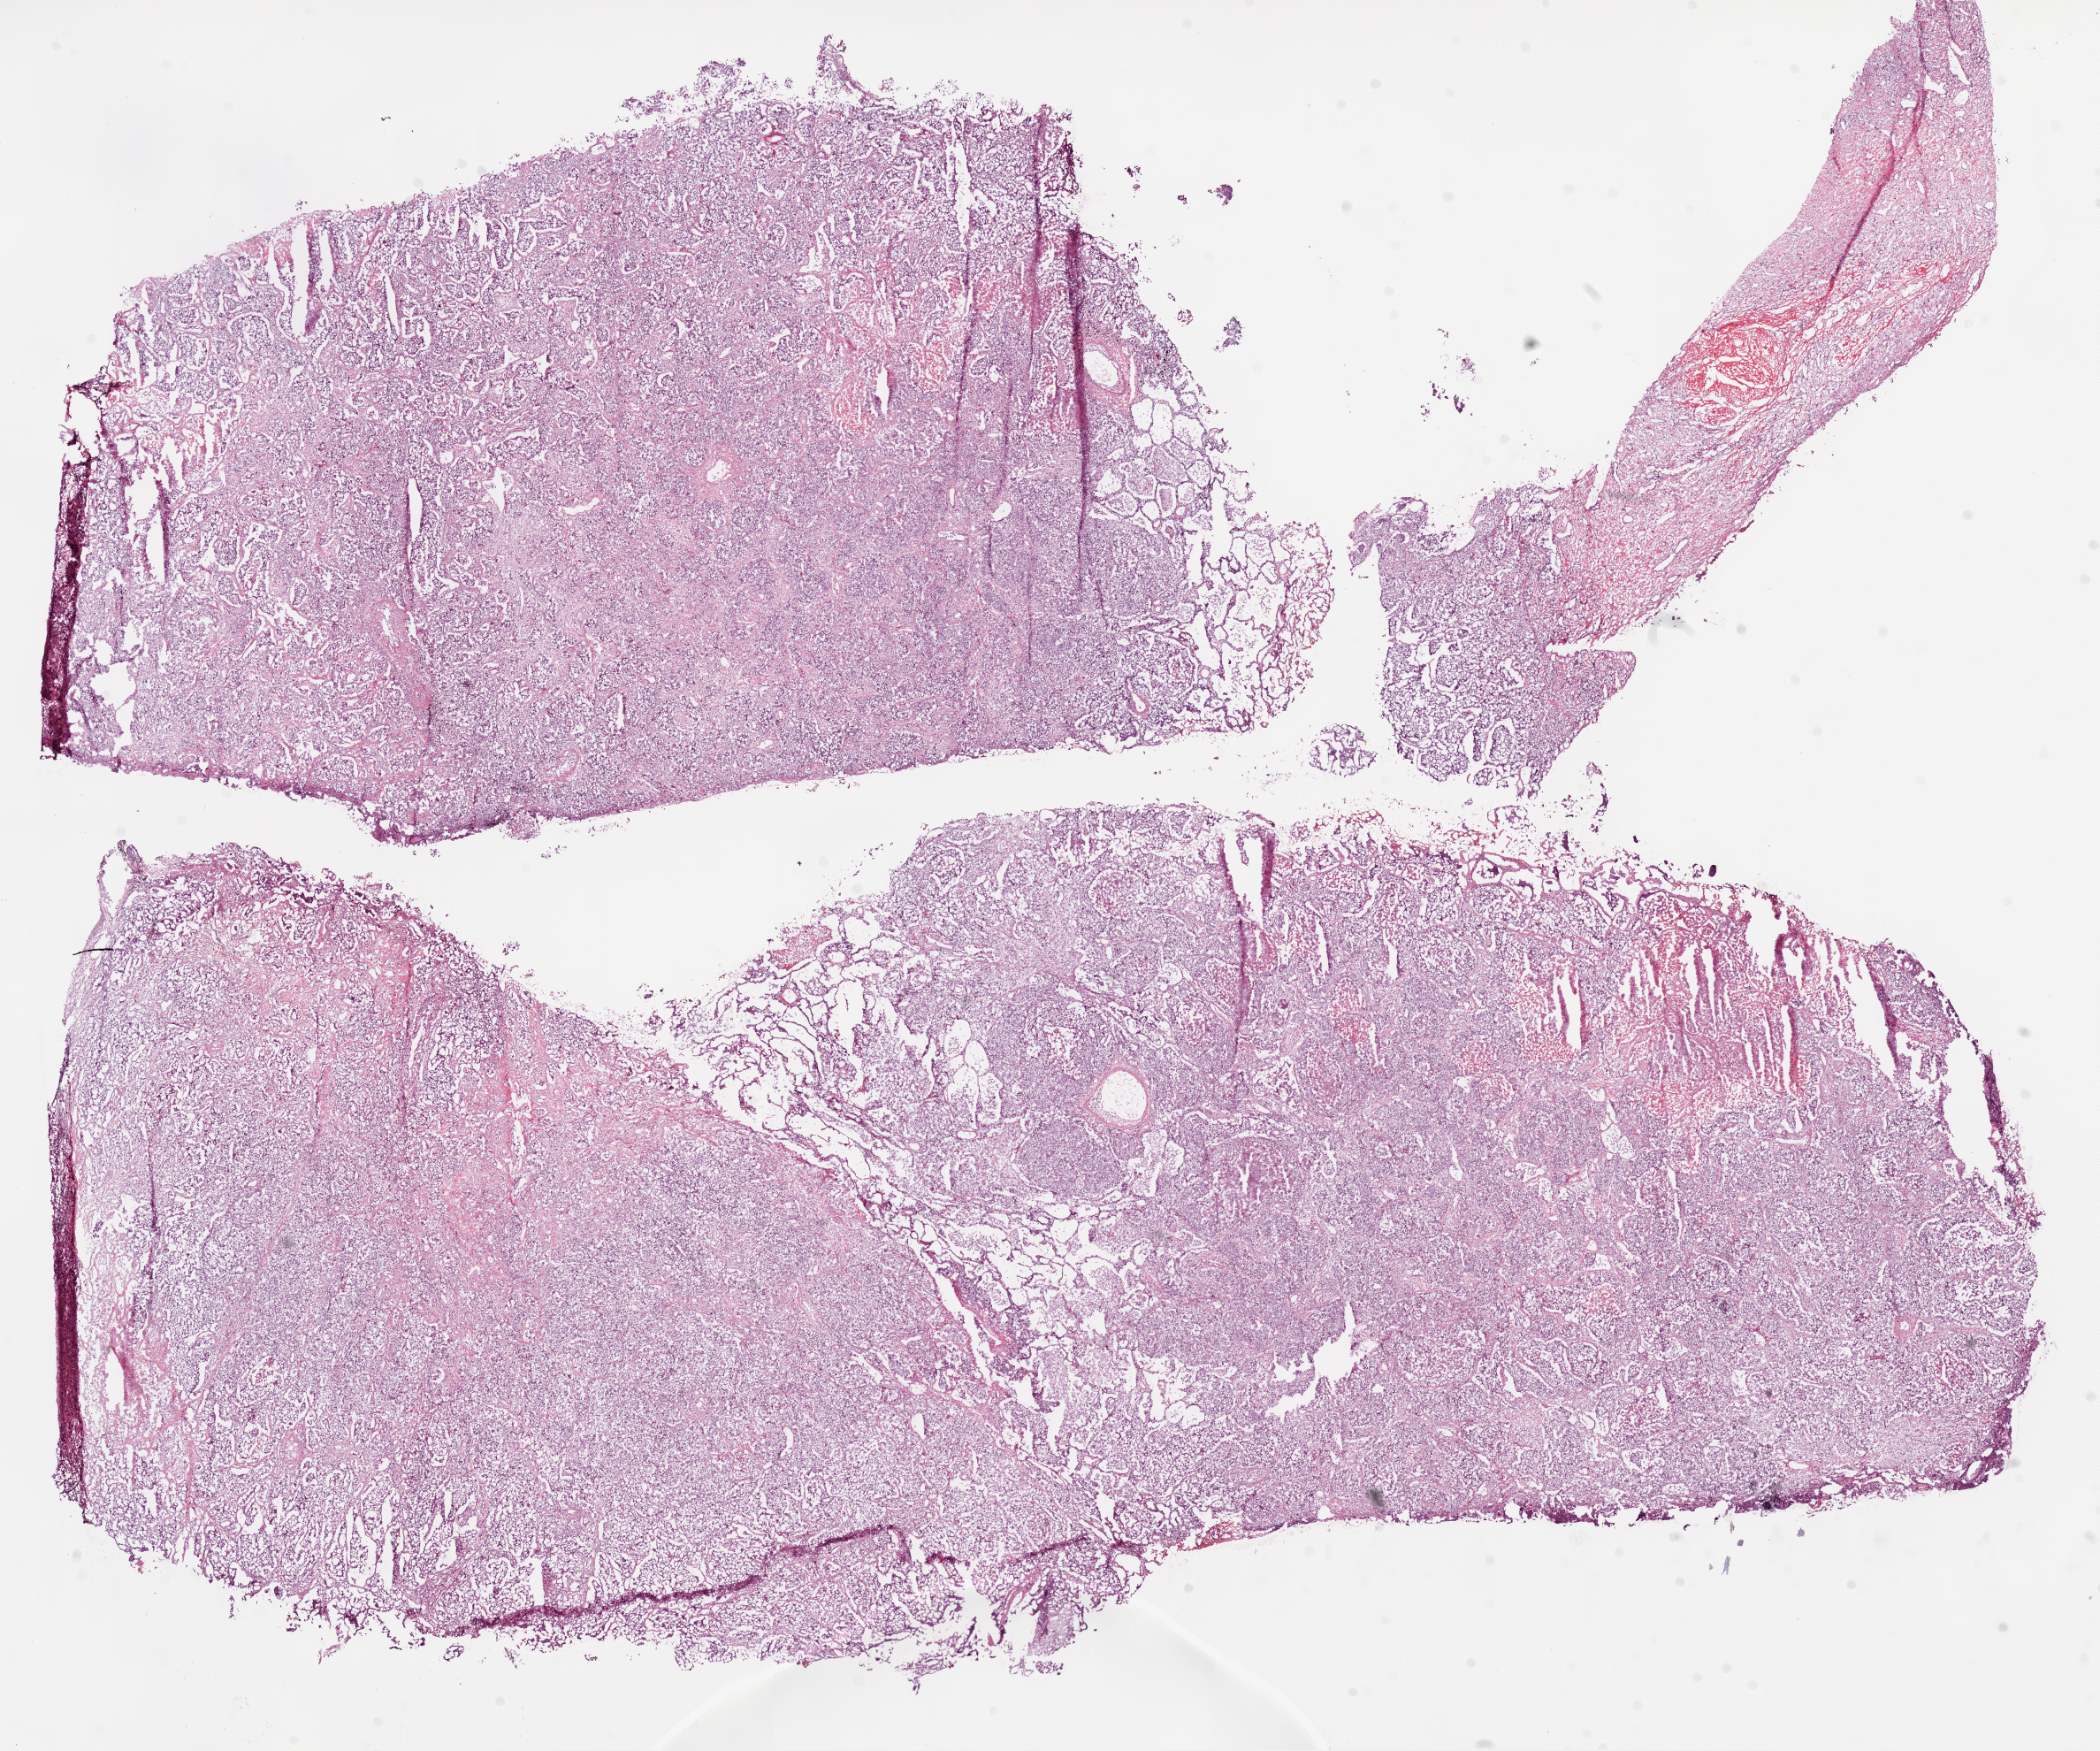
Whole-slide histology image, H&E, low-resolution overview of the scanned area, about 19.1 x 15.9 mm (acquisition: 20x scan), frozen section from the bottom of the tissue portion, sample: primary tumour, lung. Patient: female, age at initial diagnosis 70 years. Slide review estimates, as recorded: tumour cells 90%, tumour nuclei 80%, normal cells 0%, stromal cells 5%, necrosis 5%. Infiltration values recorded for this section: lymphocyte infiltration 10%, monocyte infiltration 2%, neutrophil infiltration 2%.
Histologic diagnosis: Squamous cell carcinoma, NOS. AJCC pathologic stage: IA (6th edition).